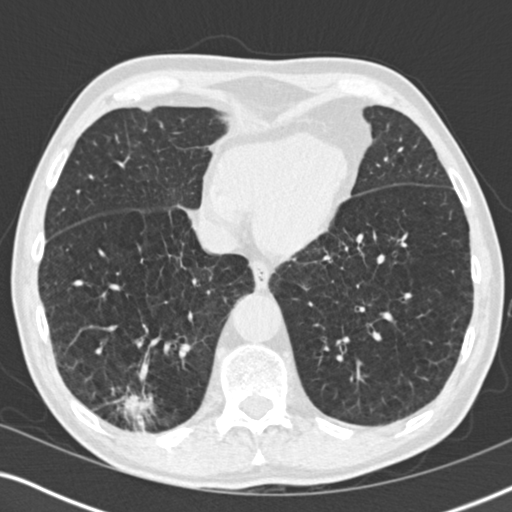
Low-dose screening chest CT, axial slice. First (baseline) screen. Lung window (W 1500 / L -600 HU). Standard (soft-tissue) reconstruction kernel (B30f). 120 kVp. Male participant, aged 64 years at enrolment. Former smoker at enrolment.
Expert reader's lesion annotation, bounding box [x1, y1, x2, y2] px = [86, 371, 179, 447]. The screening reader recorded 3 non-calcified nodules or masses ≥4 mm on this exam; which of them this box marks is not recorded. Official screen result: positive, change unspecified: nodule(s) >= 4 mm or enlarging nodule(s), mass(es), or other non-specific abnormalities suspicious for lung cancer. Participant outcome: lung cancer diagnosed 27 days after this screen — squamous cell carcinoma, NOS, right lower lobe, moderately differentiated (G2), stage IV (AJCC 6th edition), 40 mm at pathology.